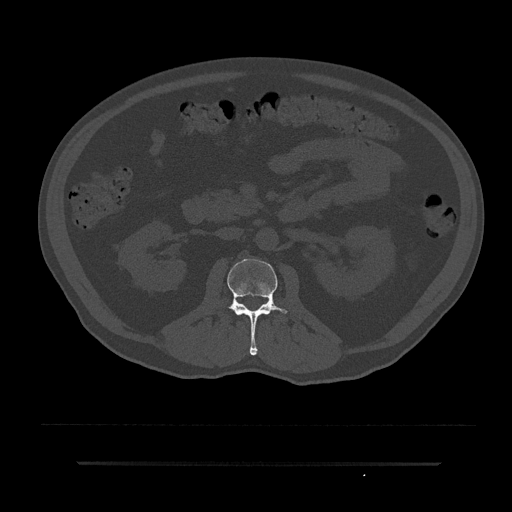
CT including the spine, one axial slice. Position 72 of 797 along the scan axis. Reconstruction kernel Br40s/3. 120 kVp. Bone window (W 1800 / L 400 HU). 0.5 mm slice thickness. 512 × 512 image matrix, field of view 464 × 464 mm. Patient: male, 59 years. From the clinical record (not read from this slice): primary cancer: bile ducts.
Structures marked on this image (semi-automatic segmentation, software-assisted and operator-edited):
- L2 vertebra: box from (x=227, y=259) to (x=288, y=355) px